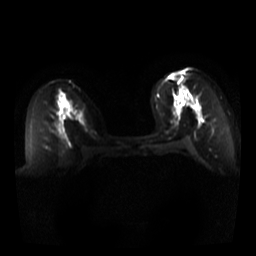
Breast MRI, one axial slice. Position 19 of 44 along the scan axis. Diffusion-weighted series; image 2 of 4 stored at this slice position (different b-values; order by instance number). 3 T. 5 mm slice thickness. 256 × 256 image matrix. Female patient.
Structures marked on this image (manually delineated by an expert):
- tumour on diffusion-weighted imaging: bounding box (x1, y1, x2, y2) in pixels: (182, 99, 197, 109)